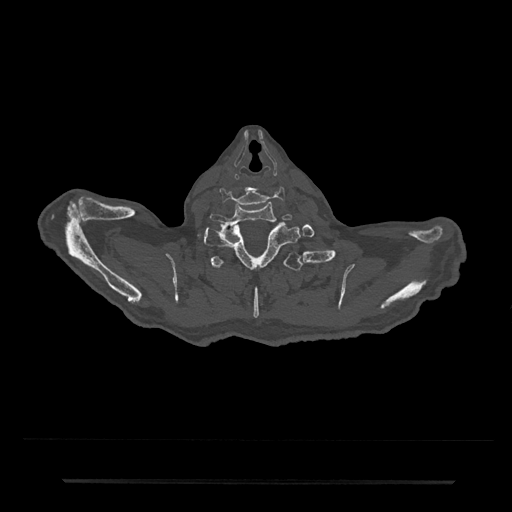
CT including the spine, one axial slice. Position 722 of 797 along the scan axis. 120 kVp. Bone window (W 1800 / L 400 HU). 0.5 mm slice thickness. 512 × 512 image matrix. Patient: male, 74 years. From the clinical record (not read from this slice): primary cancer: prostate.
Structures marked on this image (semi-automatically segmented with operator editing):
- T1 vertebra: bounding box [x1, y1, x2, y2] px = [203, 221, 300, 268]
- T2 vertebra: [210, 251, 314, 319]